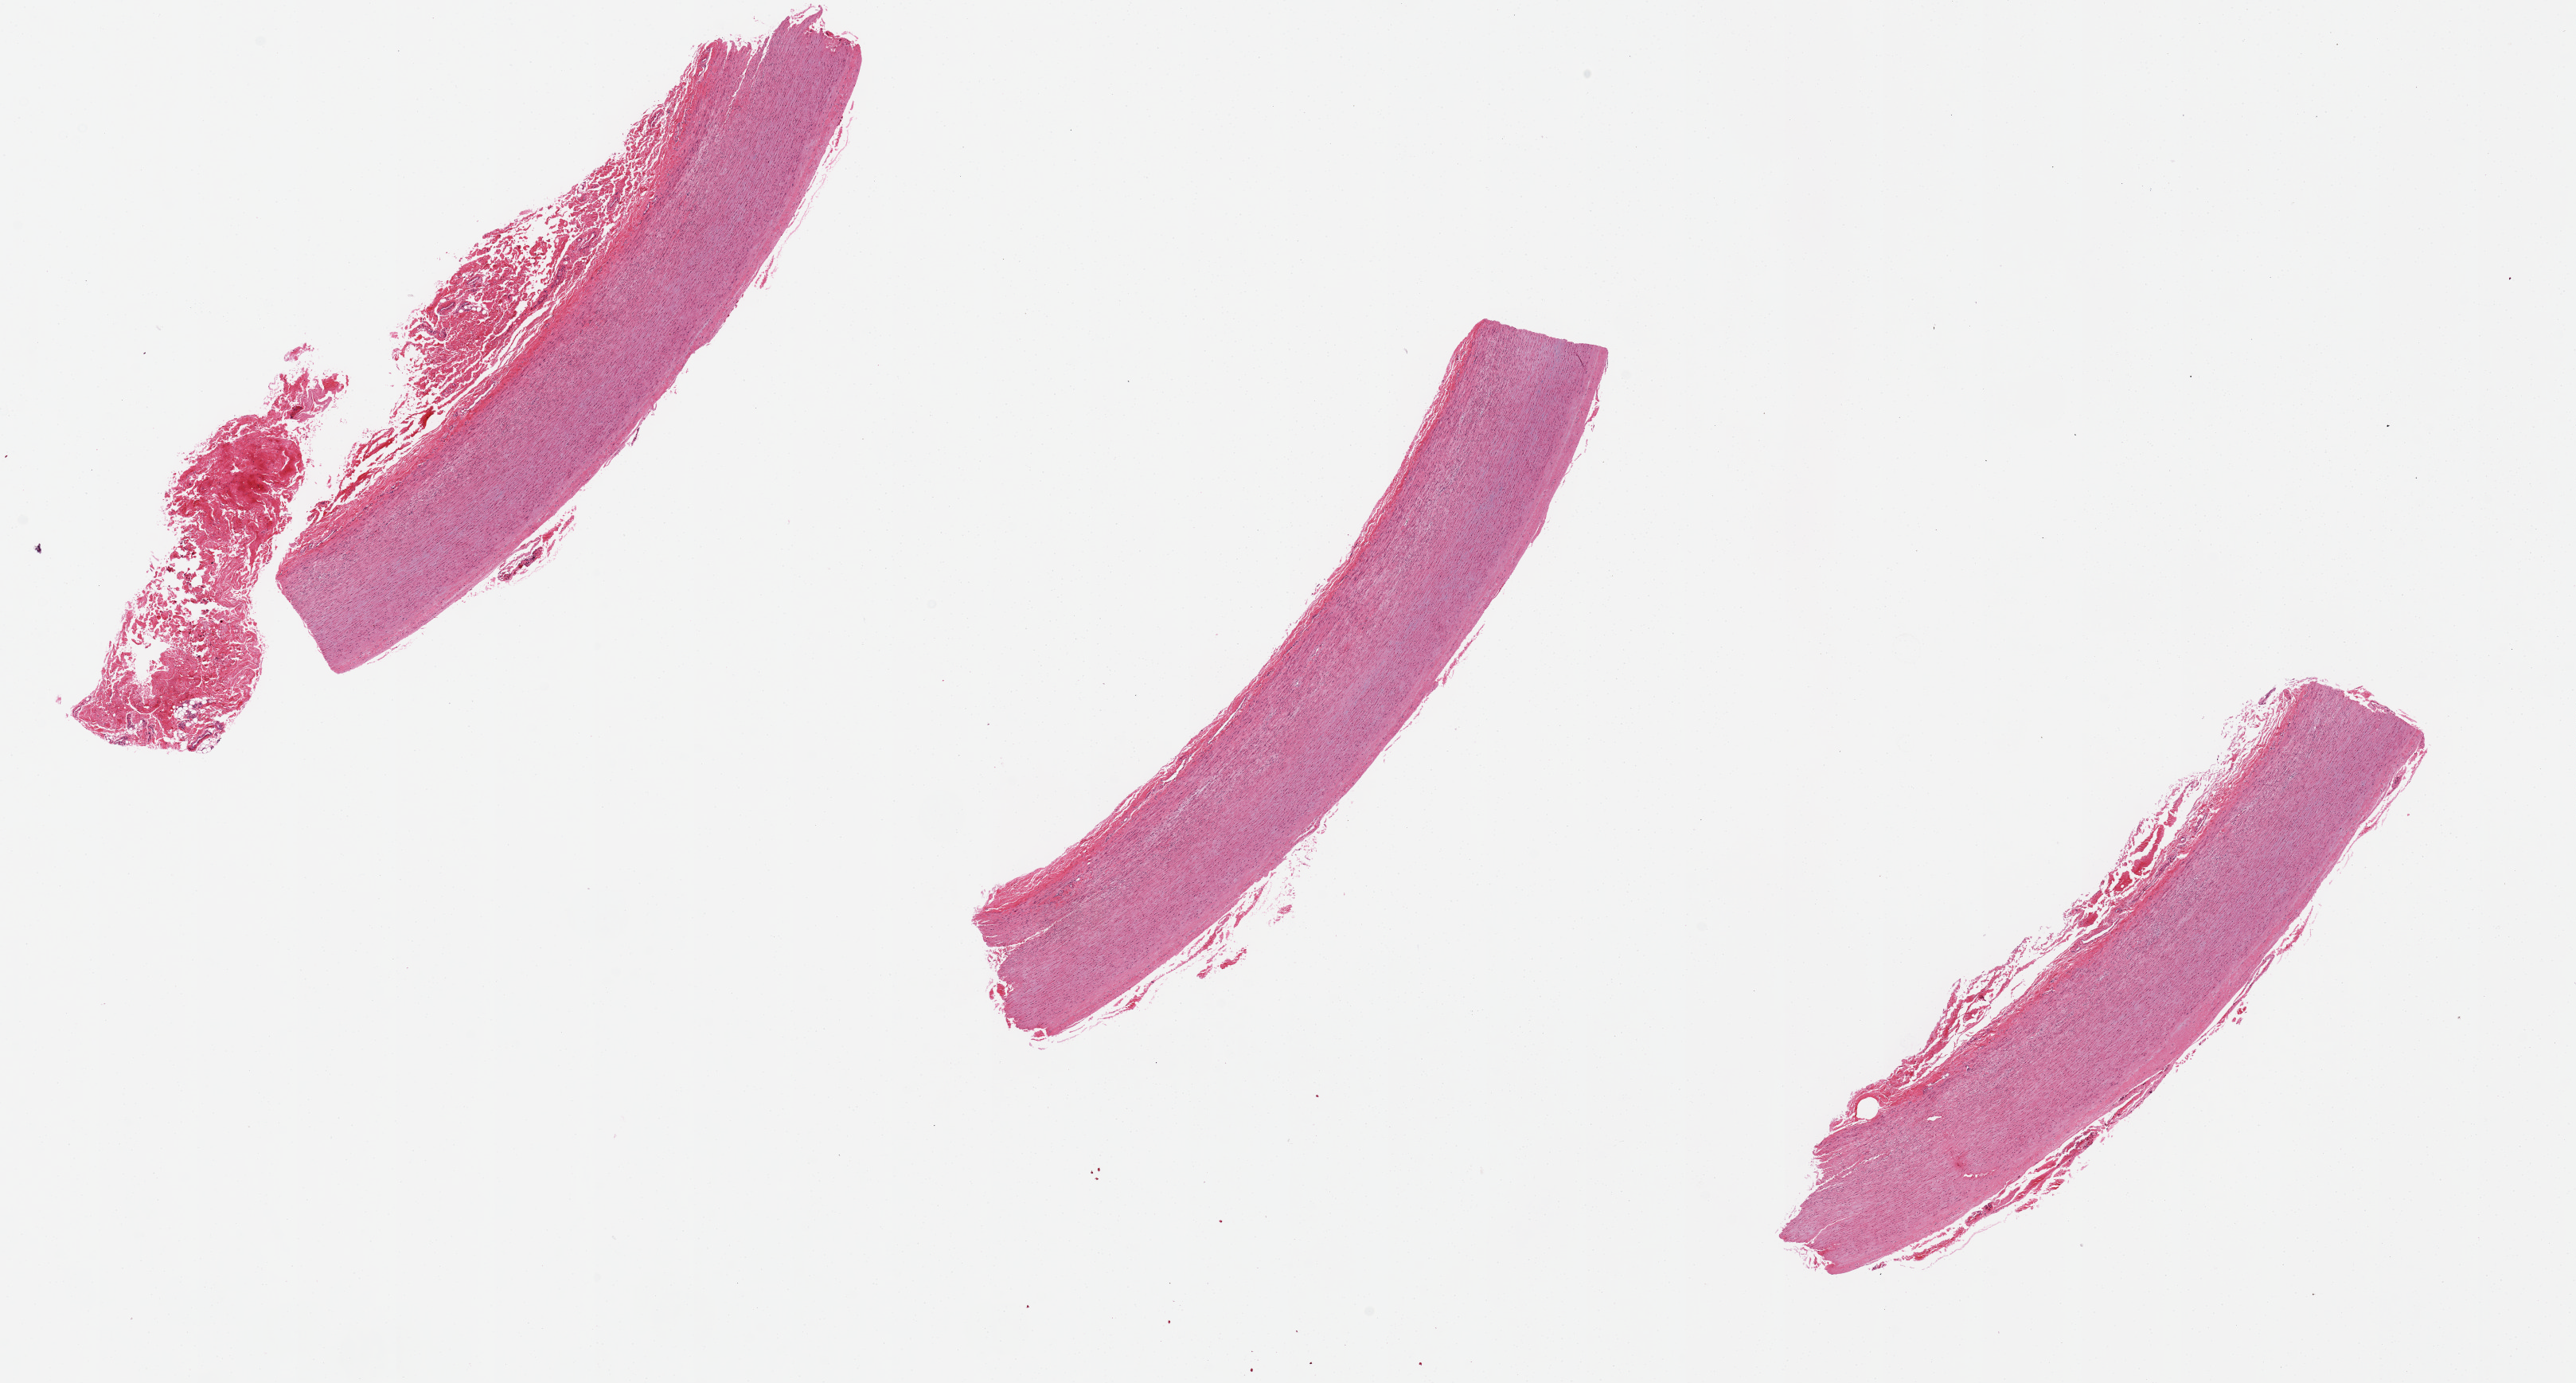
Digitized H&E-stained section — whole scanned area (about 25.6 x 13.7 mm) shown as a low-resolution overview, PAXgene-fixed paraffin-embedded (PFPE) section, sampled site (target tissue): aorta, donor tissue sample.
Reviewer comment on this tissue sample: Endothelium totally sloughed.